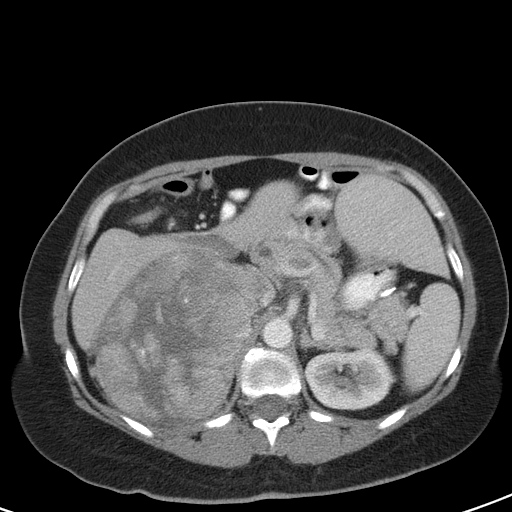
Contrast-enhanced abdominal CT, one axial slice. Slice 70 of 126 in the series (ordered by position). 120 kVp. Intravenous contrast given. Soft-tissue window (W 400 / L 40 HU). 512 × 512 image matrix. Patient: female, 51 years. Case-level facts recorded for this patient, not image findings: diagnosis: adrenocortical carcinoma; tumour side: right adrenal.
Structures marked on this image (semi-automatically segmented with operator editing):
- mass: box from (x=97, y=252) to (x=261, y=421) px